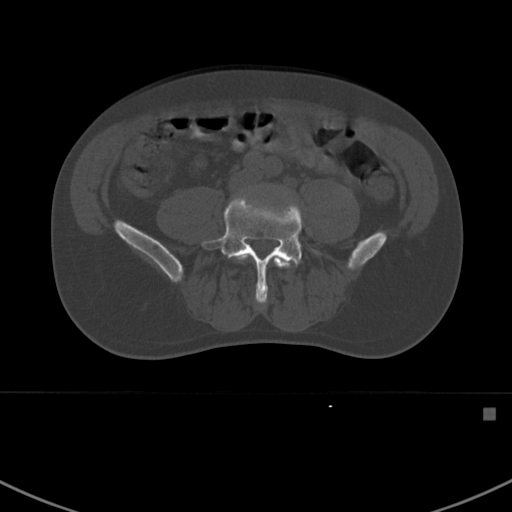
CT including the spine, one axial slice; slice 226 of 412 in the series (ordered by position); reconstruction kernel Br40s; bone window (W 1800 / L 400 HU); 1.5 mm slice thickness; 512 × 512 image matrix, field of view 358 × 358 mm. Patient: male, 59 years. From the clinical record (not read from this slice): primary cancer: prostate.
Outlined on this slice (semi-automatic segmentation, software-assisted and operator-edited):
- L4 vertebra: box from (x=237, y=253) to (x=291, y=293) px
- L5 vertebra: (x=201, y=195)–(x=302, y=304)